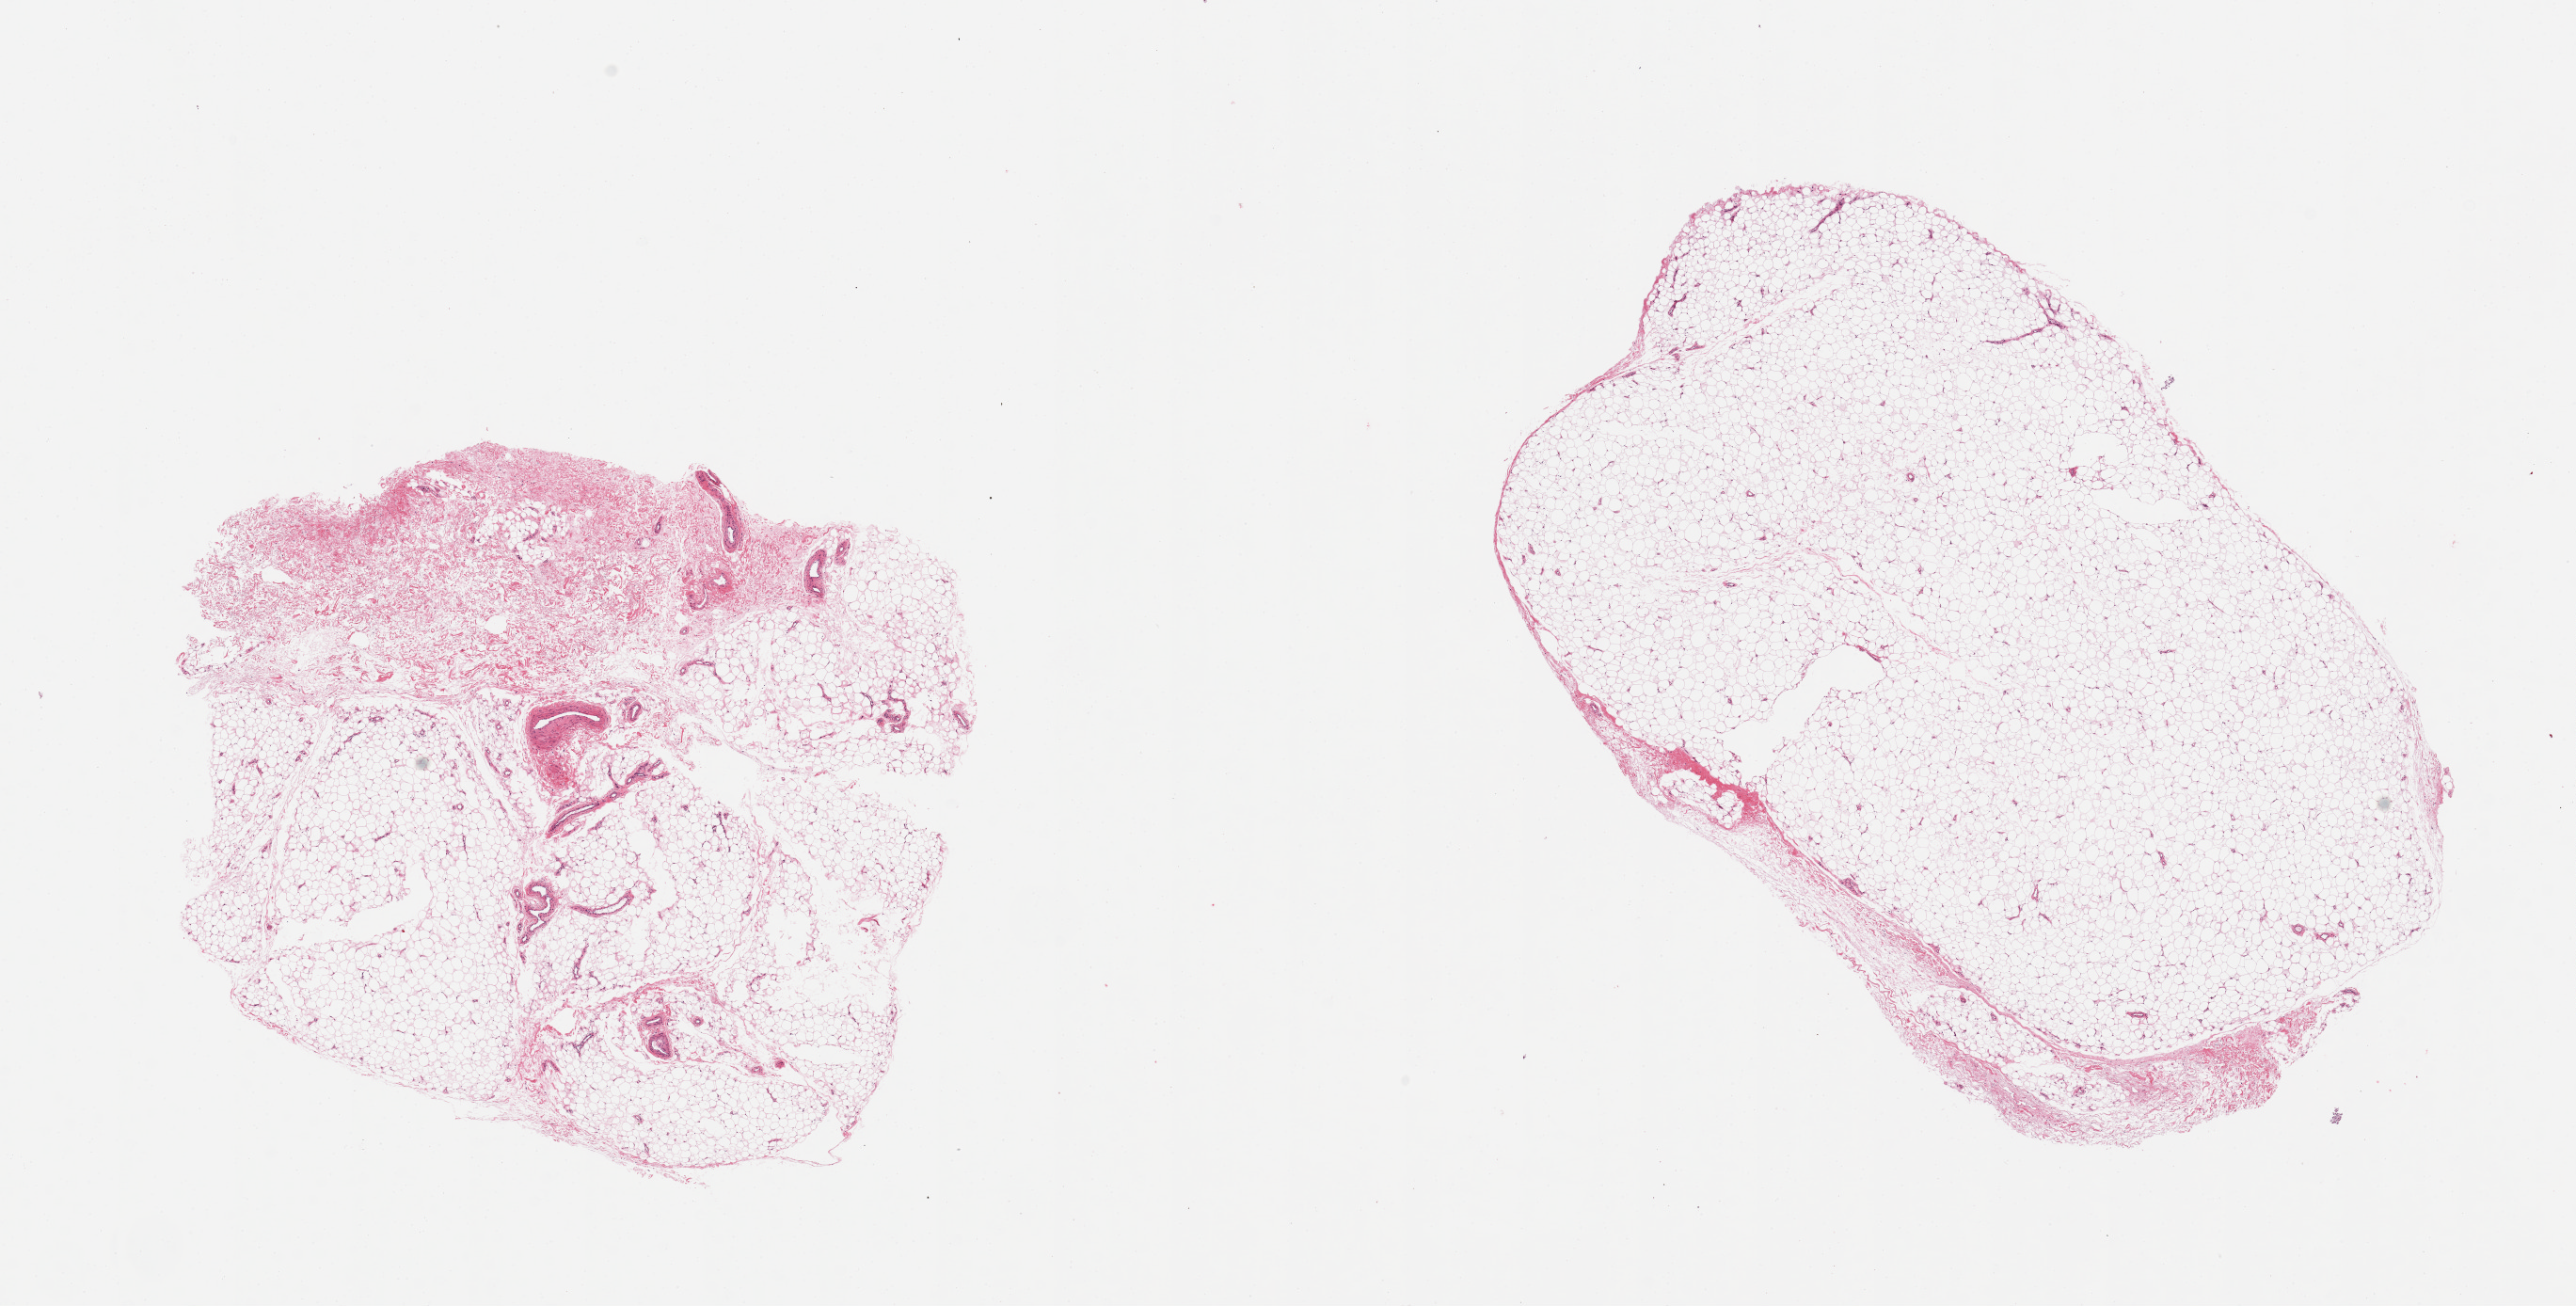
H&E whole-slide image, brightfield — shown as a low-resolution overview of the whole scanned area (about 21.7 x 11.0 mm, acquisition: 20x scan). PAXgene-fixed paraffin-embedded (PFPE) section. Section of adipose tissue (target tissue). Donor tissue sample. Male donor.
Pathologist's review note for this sample: 2 pieces; fat with up to 20% connective tissue/vessels.